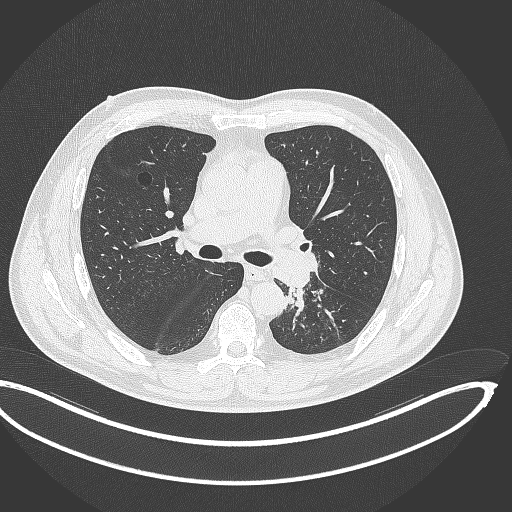
Chest CT, one axial slice; position 213 of 362 along the scan axis; lung window (W 1500 / L -600 HU); 512 × 512 image matrix, field of view 442 × 442 mm. Patient: male, 50 years. Case-level facts recorded for this patient, not image findings: clinical TNM (as recorded): T2a N3 M0.
Outlined on this slice (rectangle marked by the reading radiologist):
- lung tumour (recorded histology: squamous cell carcinoma): bounding box (x1, y1, x2, y2) in pixels: (284, 283, 308, 309)